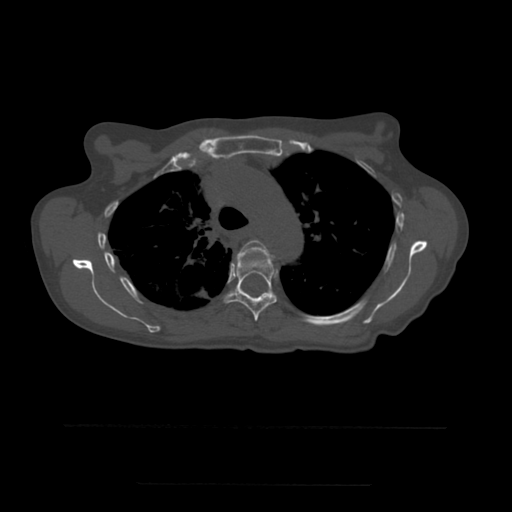
CT including the spine, one axial slice. Position 394 of 544 along the scan axis. Bone window (W 1800 / L 400 HU). 1.25 mm slice thickness. 512 × 512 image matrix, field of view 350 × 350 mm. Patient age 58 years. Case-level facts recorded for this patient, not image findings: primary cancer: lung.
Annotated regions visible in this slice (semi-automatic segmentation, software-assisted and operator-edited):
- T4 vertebra: bounding box (x1, y1, x2, y2) in pixels: (237, 240, 274, 263)
- T5 vertebra: (223, 256, 277, 322)
- T6 vertebra: (225, 294, 230, 302)